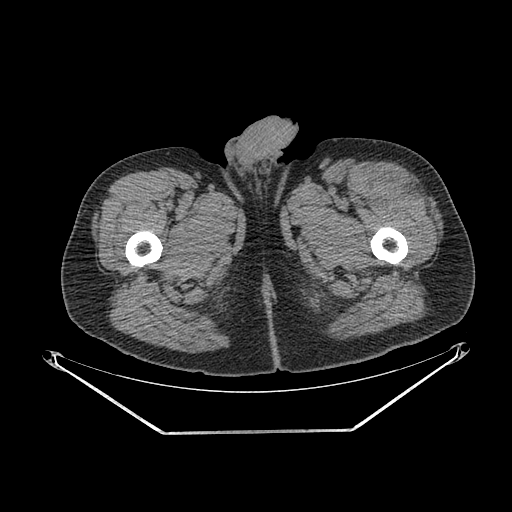
CT of an extremity soft-tissue mass (from a PET/CT study), one axial slice; slice 261 of 267 in the series (ordered by position); soft-tissue window (W 400 / L 40 HU); 3.75 mm slice thickness; 512 × 512 image matrix, field of view 500 × 500 mm. Male patient. Case-level facts recorded for this patient, not image findings: histological type: extraskeletal osteosarcoma; grade: high; site of the primary tumour: thigh.
Outlined on this slice (expert contour drawn on MRI and transferred to this co-registered scan by the dataset authors):
- gross tumour volume (mass): box from (x=379, y=174) to (x=419, y=195) px